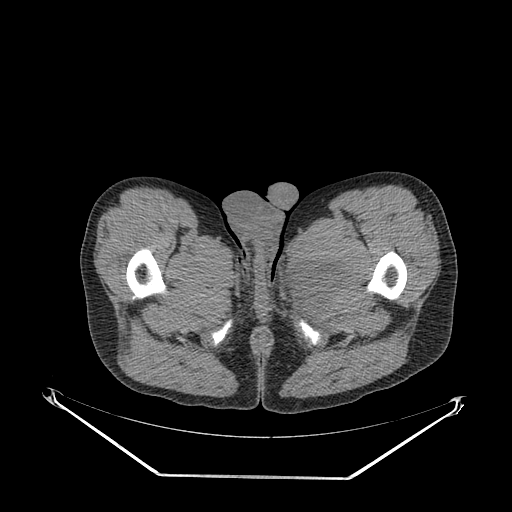
CT of an extremity soft-tissue mass (from a PET/CT study), one axial slice. Slice 42 of 267 in the series (ordered by position). Reconstruction kernel SOFT. Soft-tissue window (W 400 / L 40 HU). 512 × 512 image matrix. Male patient. Case-level facts recorded for this patient, not image findings: histological type: pleiomorphic liposarcoma; grade: high; site of the primary tumour: left thigh.
Outlined on this slice (expert contour drawn on MRI and transferred to this co-registered scan by the dataset authors):
- gross tumour volume including surrounding oedema: box from (x=288, y=256) to (x=348, y=320) px
- gross tumour volume (mass): (x=292, y=260)–(x=339, y=300)